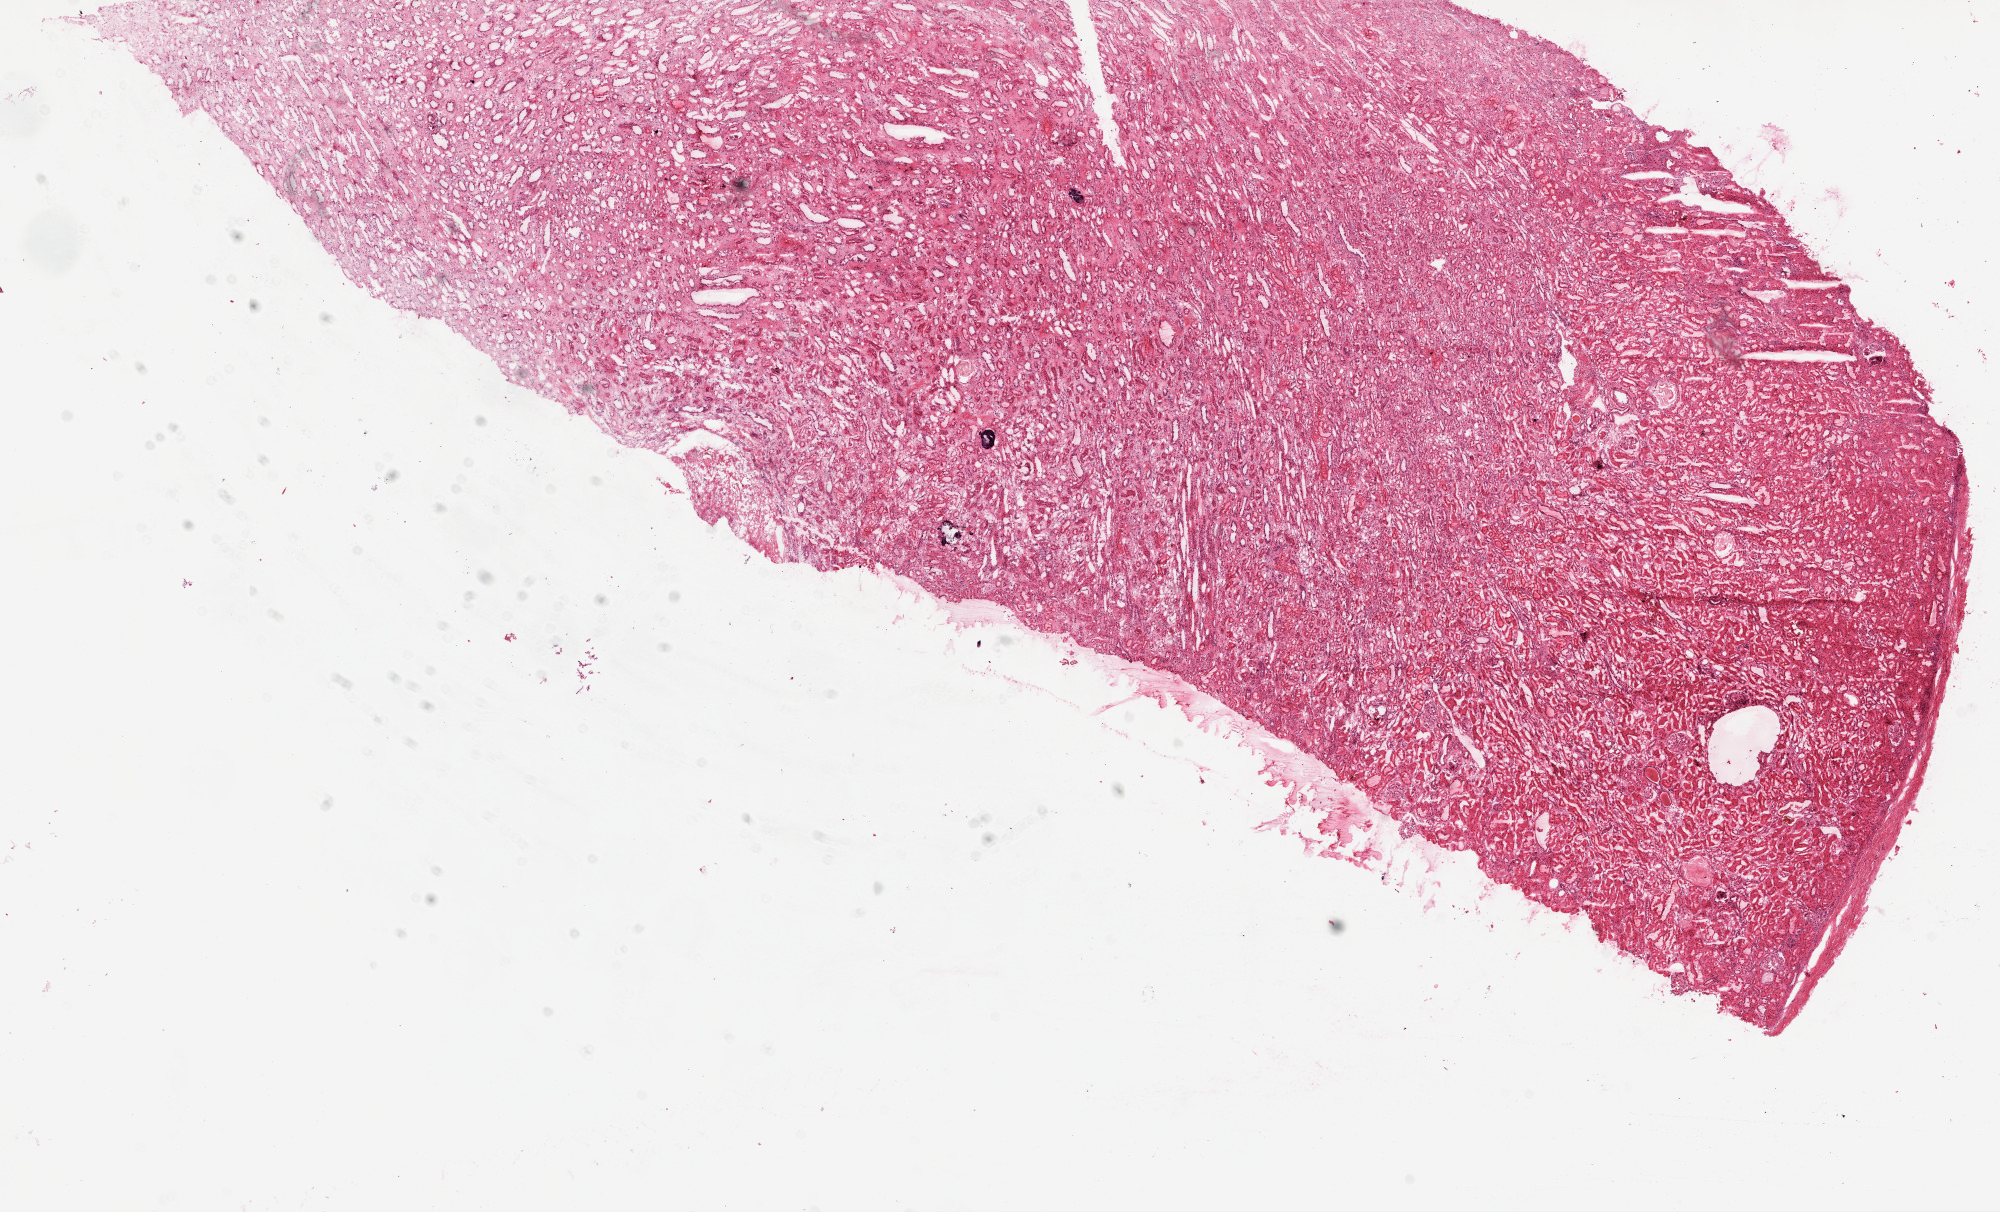
Digitized Hematoxylin and eosin (H&E) stained tissue section (whole slide) — whole scanned area (about 16.0 x 9.7 mm) shown as a low-resolution overview, frozen section from the top of the tissue portion, kidney, solid tissue normal (non-tumour tissue) sample. Female, age 65 years at initial diagnosis.
- this section: solid tissue normal sample (biorepository sample class)
- patient diagnosis: Clear cell adenocarcinoma, NOS